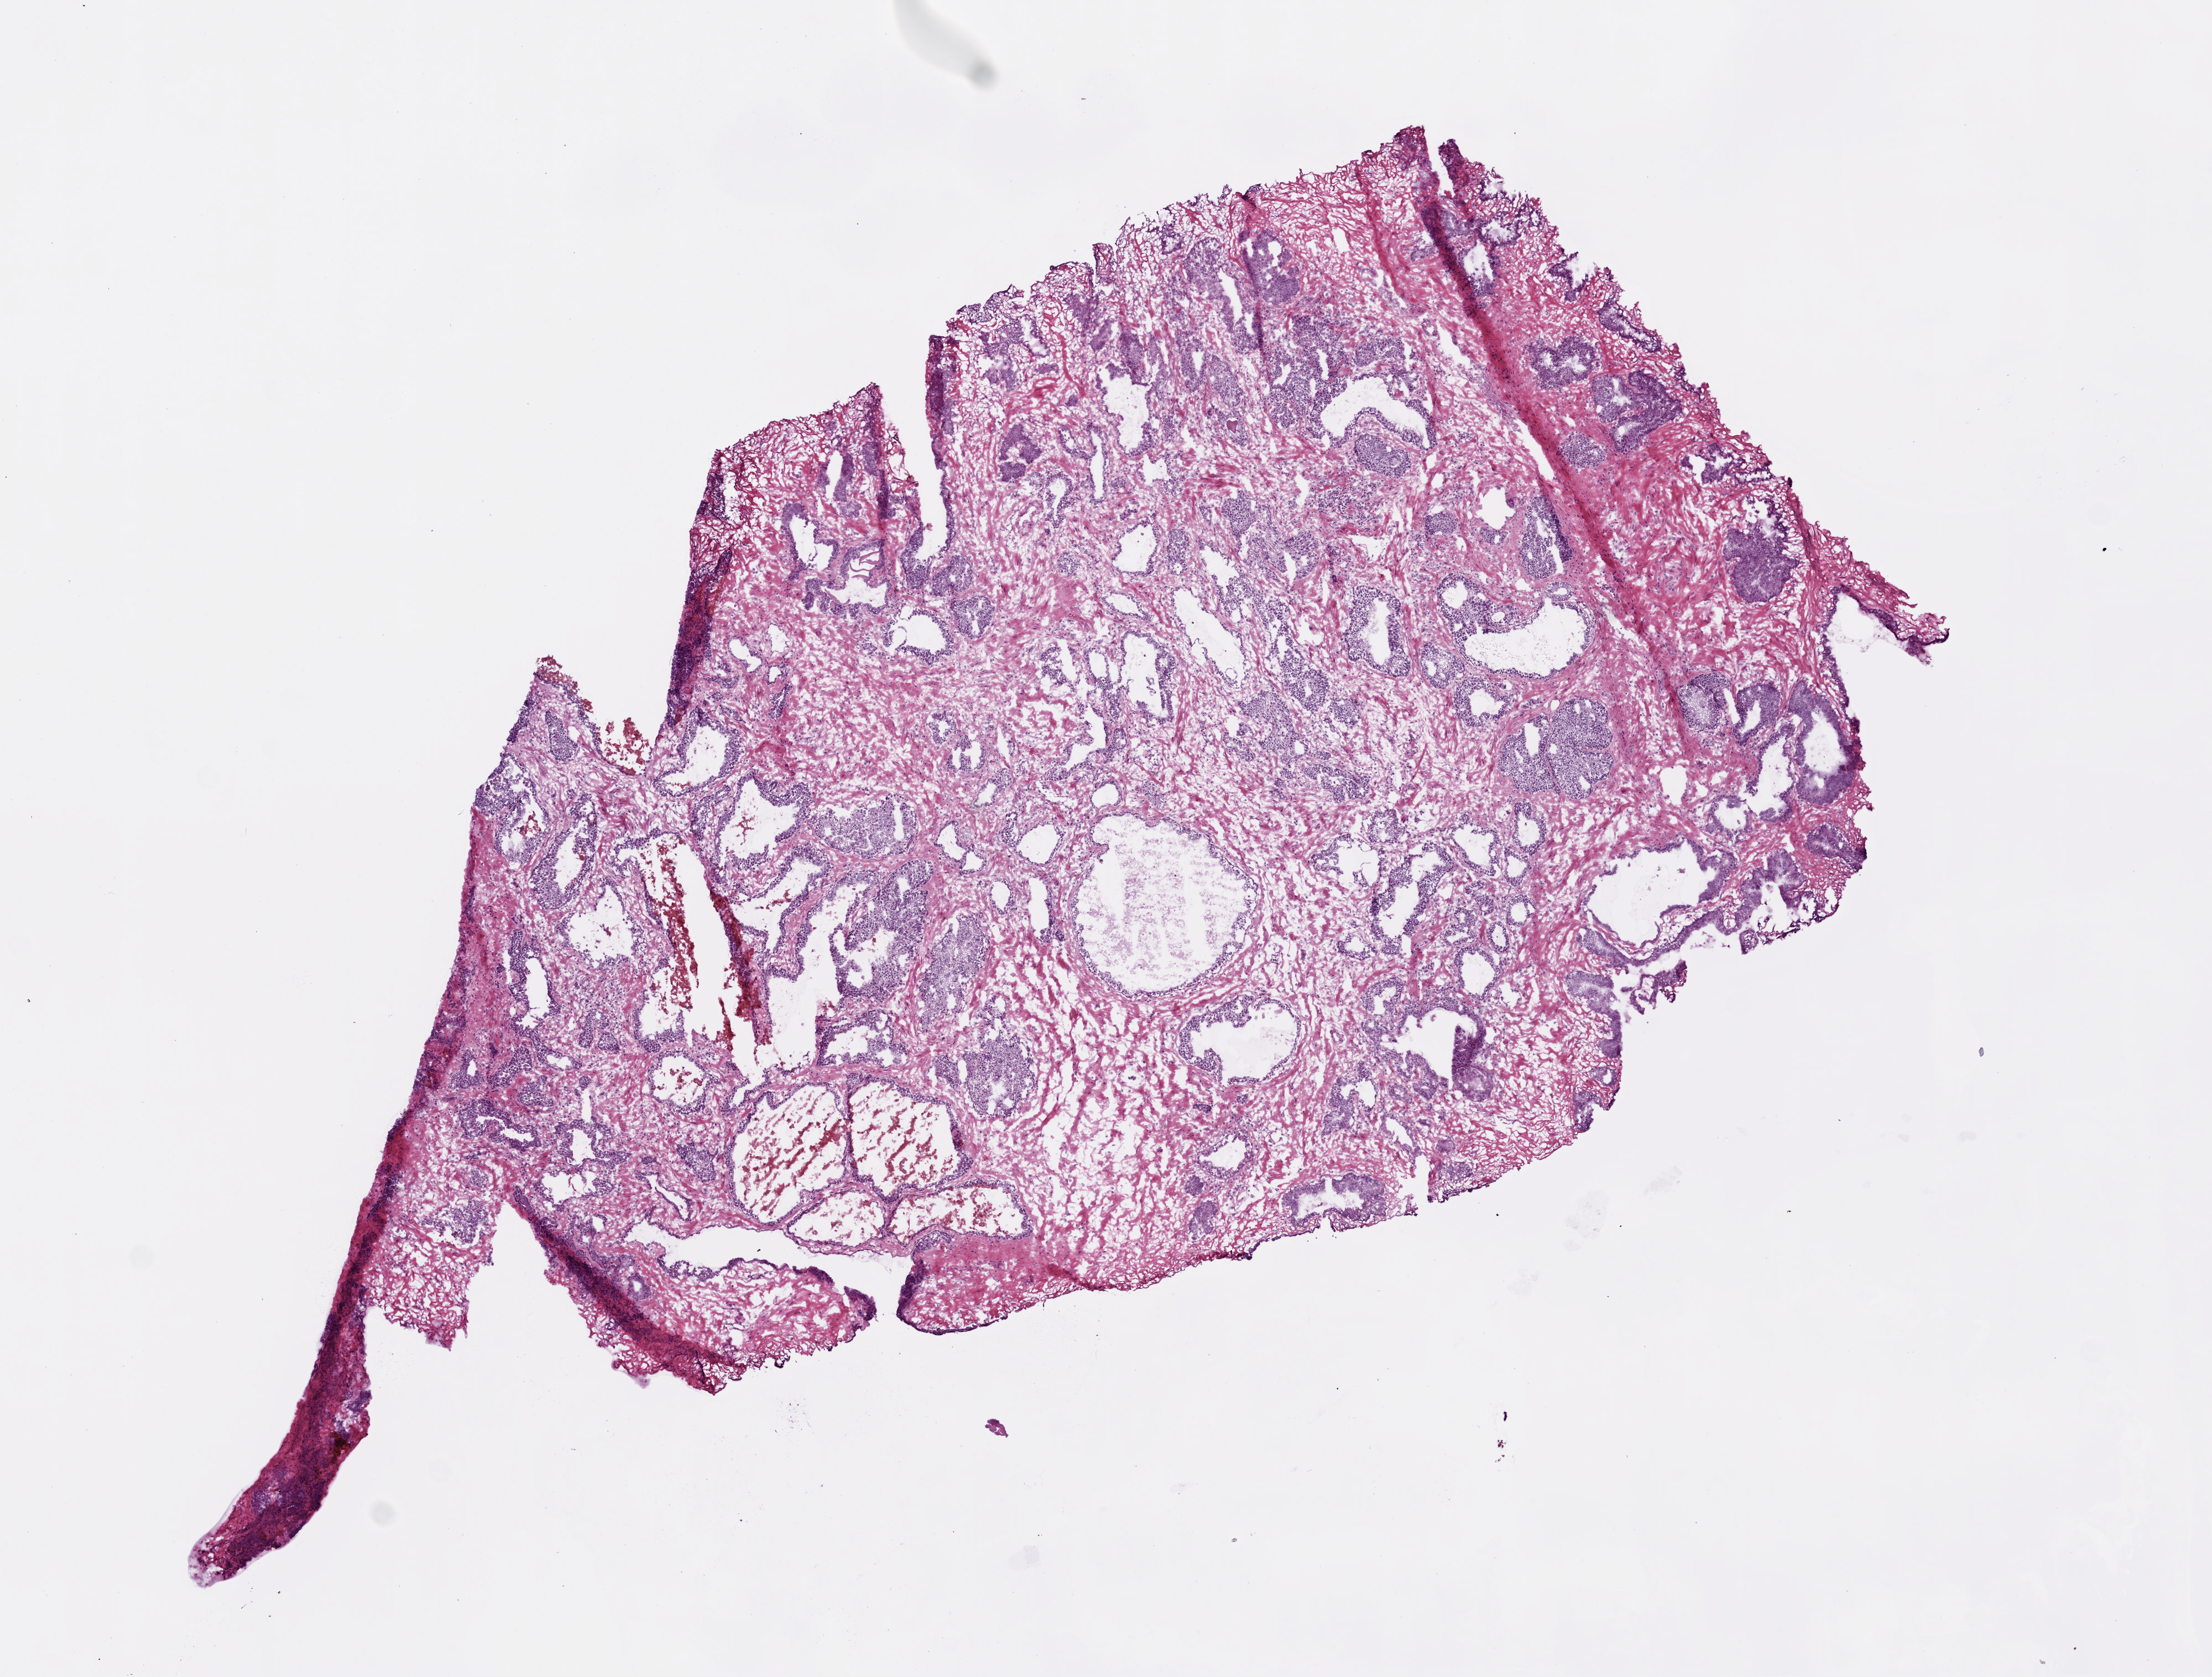
Whole-slide histology image, H&E, a low-resolution overview of the entire scanned area, about 8.0 x 6.1 mm; frozen section from the top of the tissue portion; prostate, solid tissue normal (non-tumour tissue) sample. Male, age 66 years at initial diagnosis.
• this section: solid tissue normal (non-tumour) sample from the same patient
• patient diagnosis: Acinar cell carcinoma (prostate gland)